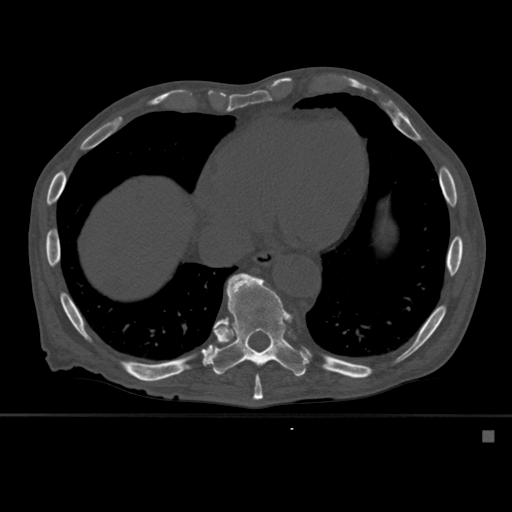
CT including the spine, one axial slice; bone window (W 1800 / L 400 HU); 1.5 mm slice thickness; 512 × 512 image matrix, field of view 373 × 373 mm. Patient: male, 78 years. From the clinical record (not read from this slice): primary cancer: prostate.
Structures marked on this image (semi-automatically segmented with operator editing):
- T10 vertebra: bounding box (x1, y1, x2, y2) in pixels: (205, 273, 308, 377)
- T9 vertebra: (253, 373, 263, 401)